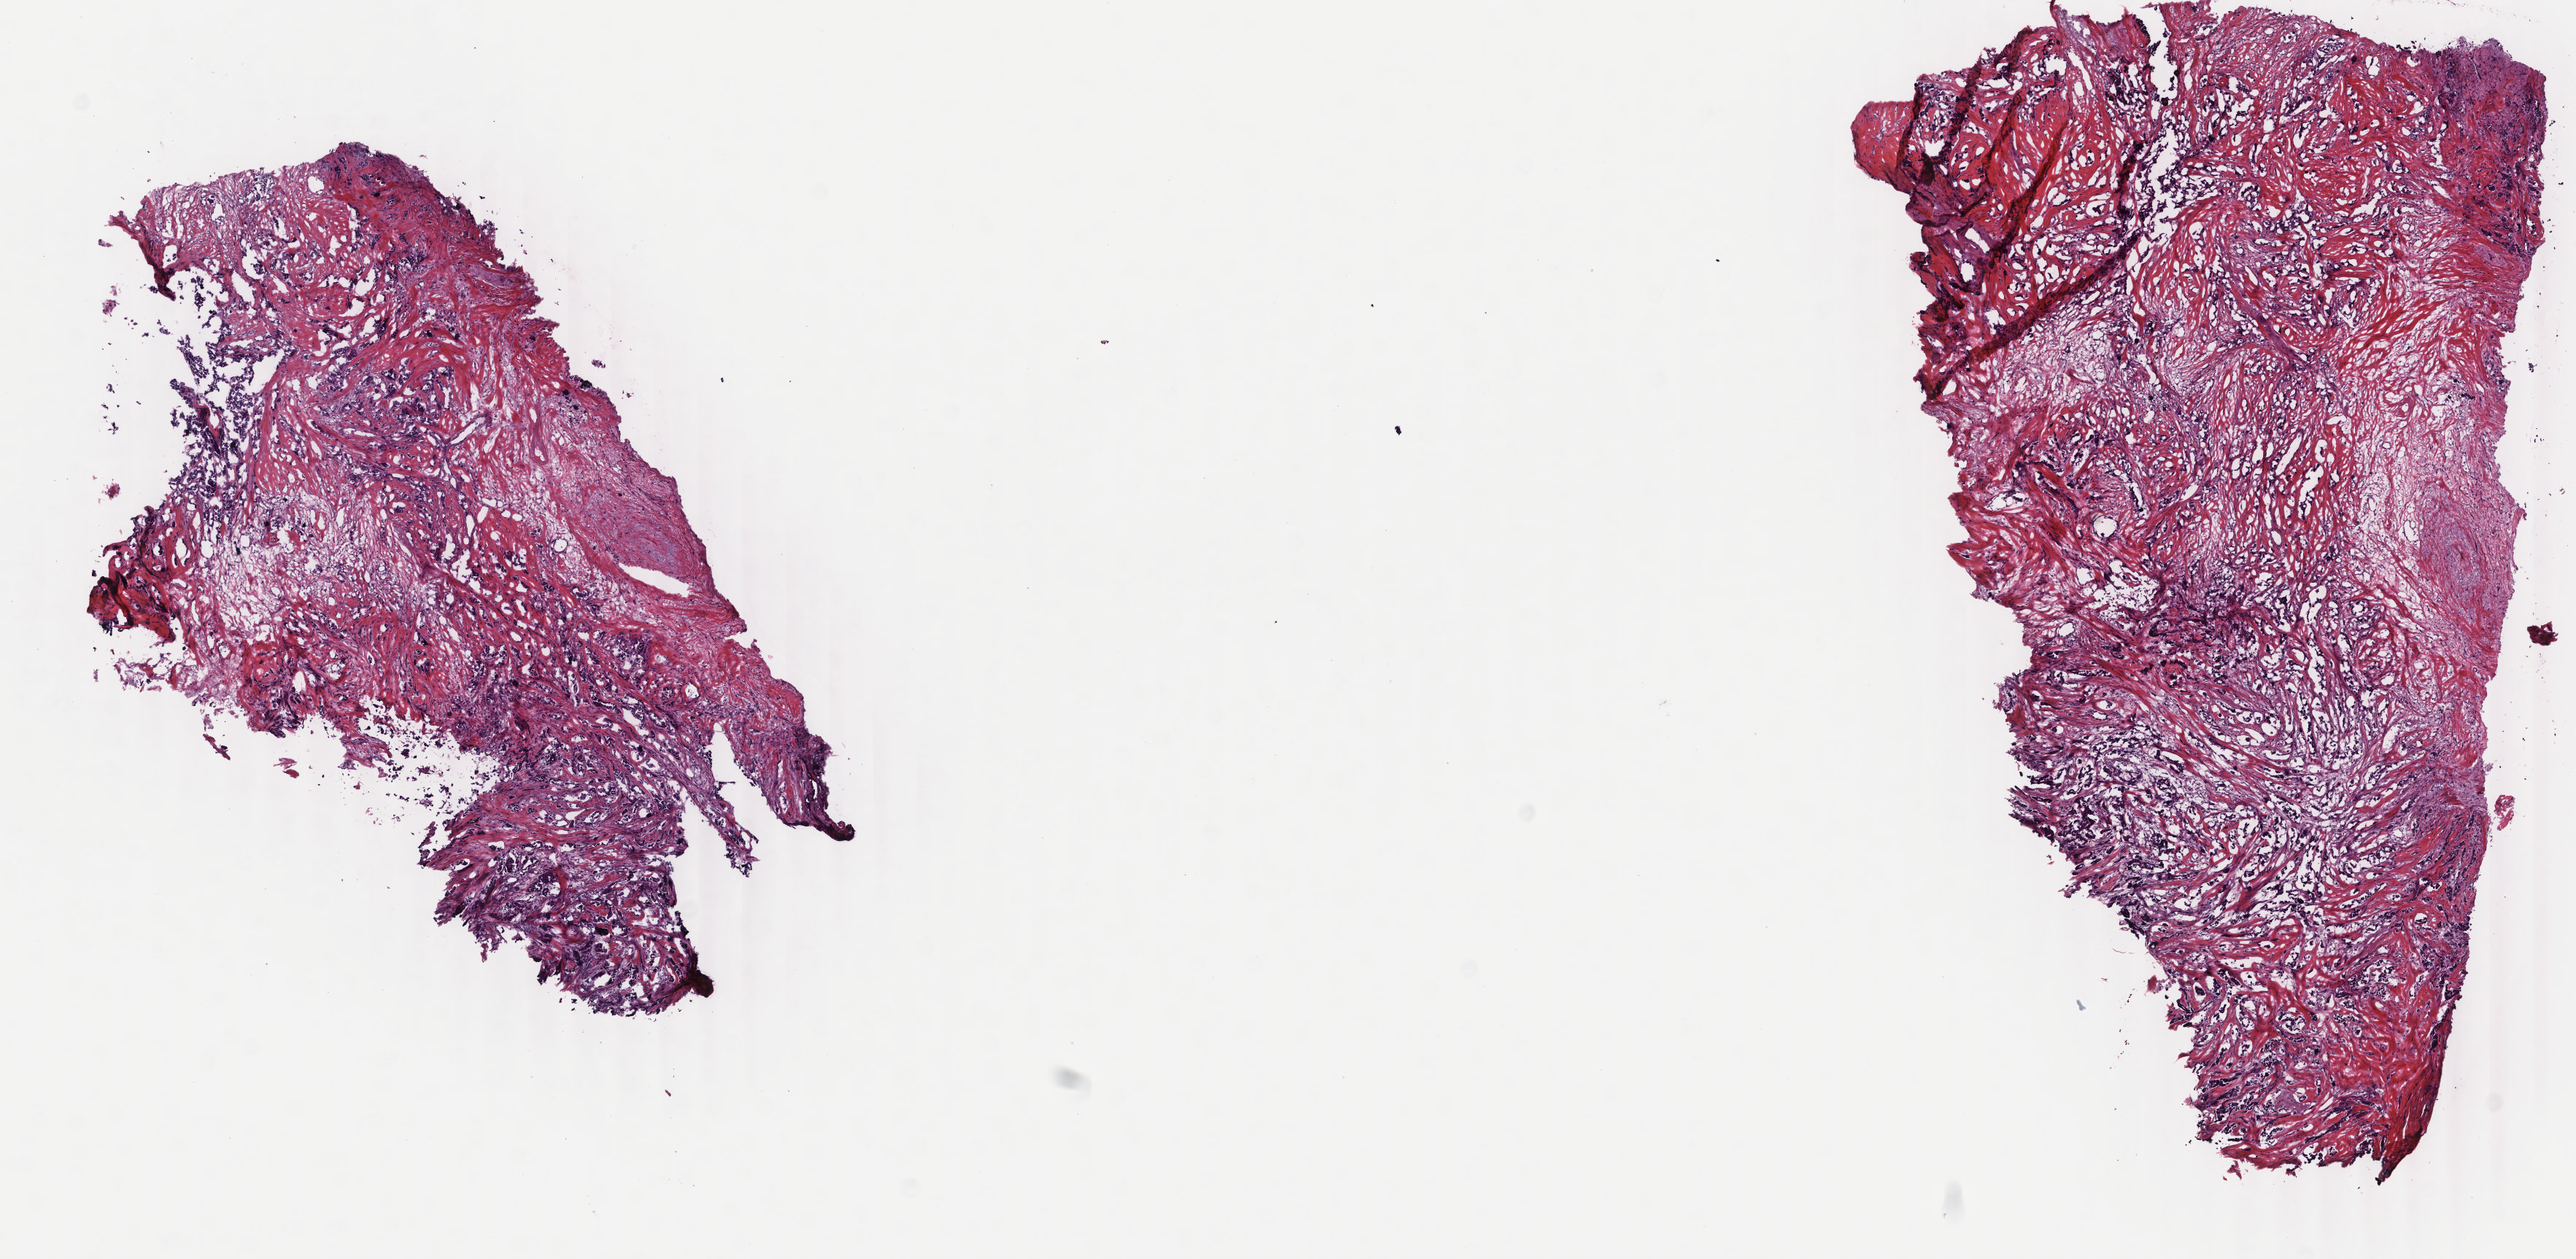
H&E-stained whole-slide image — low-resolution overview of the scanned area, about 14.0 x 6.9 mm (acquisition: 40x scan). Frozen section from the top of the tissue portion. Primary tumour sample from the breast. Patient: female, age at initial diagnosis 50 years.
Pathologic diagnosis: Infiltrating duct carcinoma, NOS.